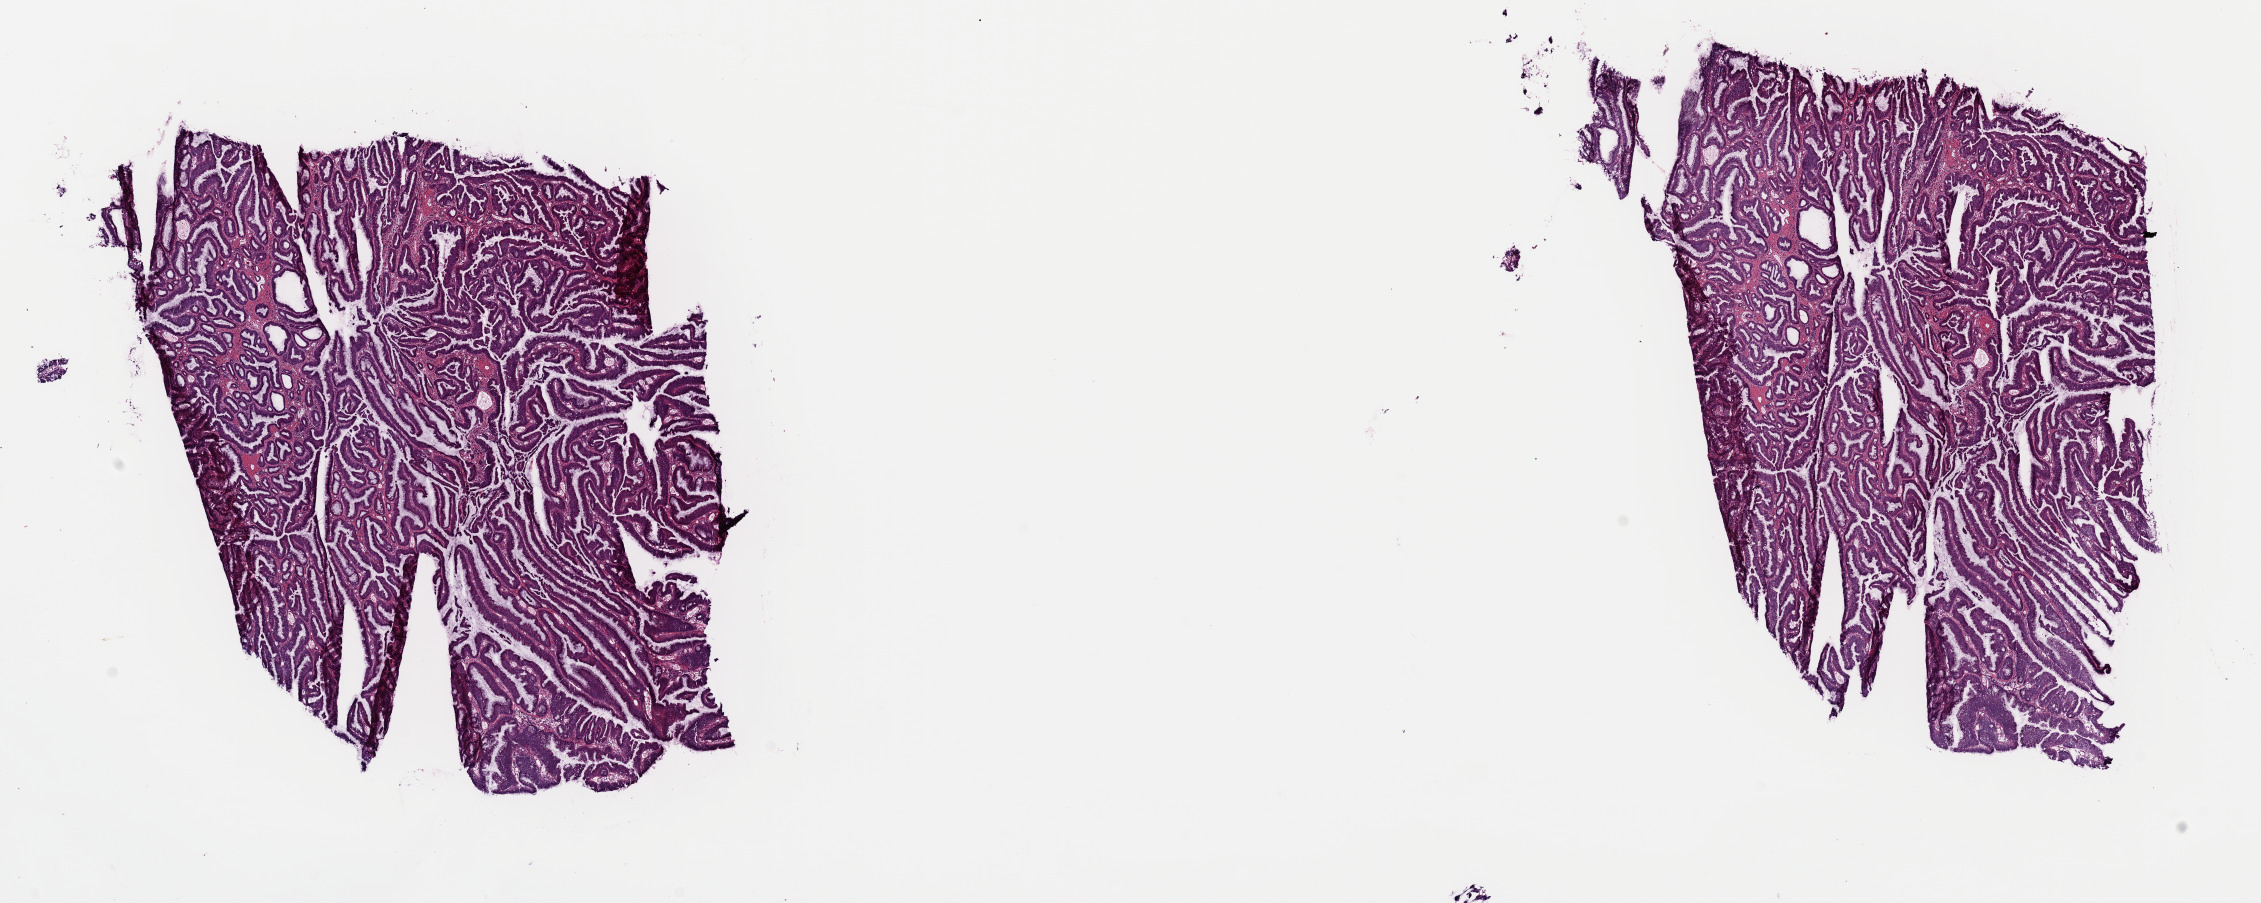
Whole-slide histology image, Hematoxylin and eosin (H&E) stained, whole scanned area (about 17.9 x 7.1 mm) shown as a low-resolution overview. Frozen section from the top of the tissue portion. Colon, primary tumour sample. Female patient; age at initial diagnosis 54 years. Composition of this section per pathologist review: tumour cells 70%, tumour nuclei 90%, normal cells 0%, stromal cells 29%, necrosis 1%. Infiltration values recorded for this section: lymphocyte infiltration 5%, monocyte infiltration 0%, neutrophil infiltration 0%.
Lymph nodes positive (case pathology): 0 of 28 examined. AJCC pathologic stage: I (7th edition). Histologic diagnosis: Adenocarcinoma, NOS.